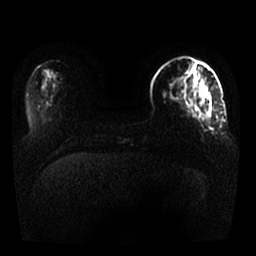
Breast MRI, one axial slice. Slice 7 of 25 in the series (ordered by position). Diffusion-weighted series; image 2 of 4 stored at this slice position (different b-values; order by instance number). 1.5 T. 4 mm slice thickness. 256 × 256 image matrix, field of view 330 × 330 mm. Female patient.
Outlined on this slice (expert manual segmentation):
- tumour on diffusion-weighted imaging: bounding box (x1, y1, x2, y2) in pixels: (202, 84, 208, 91)